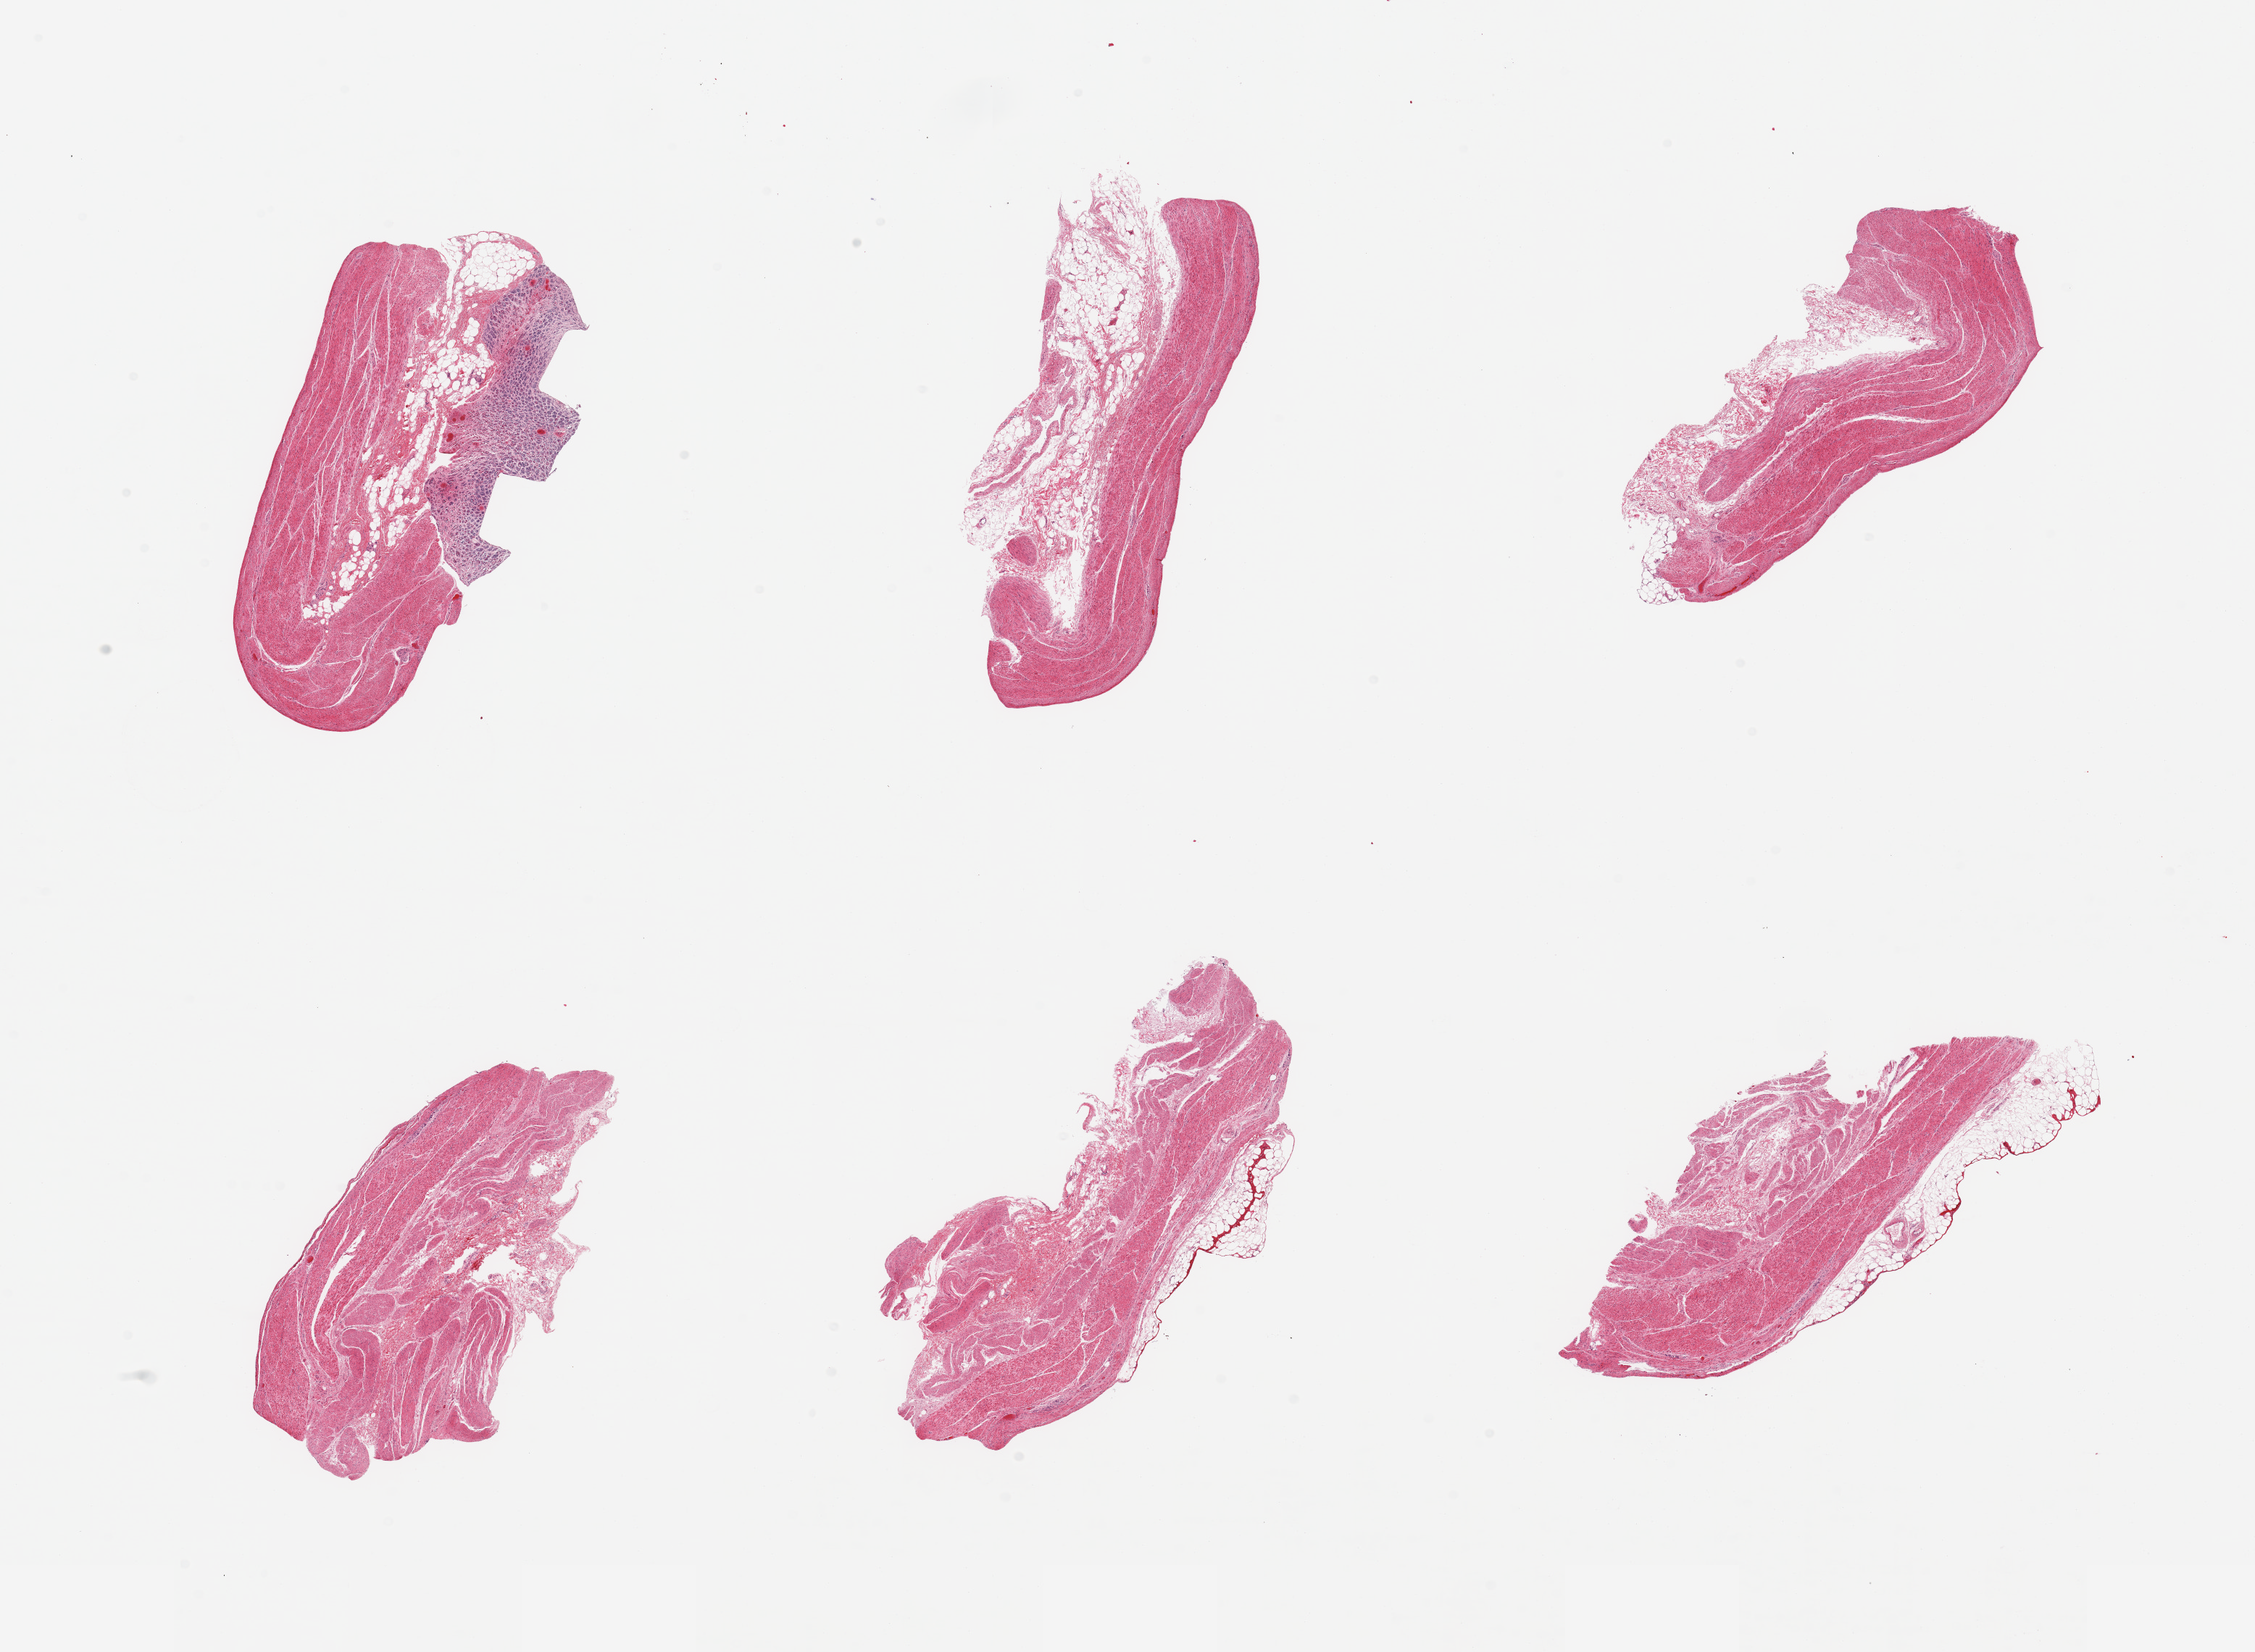
Digitized haematoxylin and eosin-stained section — a low-resolution overview of the entire scanned area, about 24.6 x 18.0 mm (acquisition: 20x scan), PAXgene-fixed paraffin-embedded (PFPE) section, target tissue: stomach, donor tissue sample. Donor: male.
Review note (as recorded): 6 pieces; one piece with fragment of autolyzed gastric mucosa and well preserved muscularis.